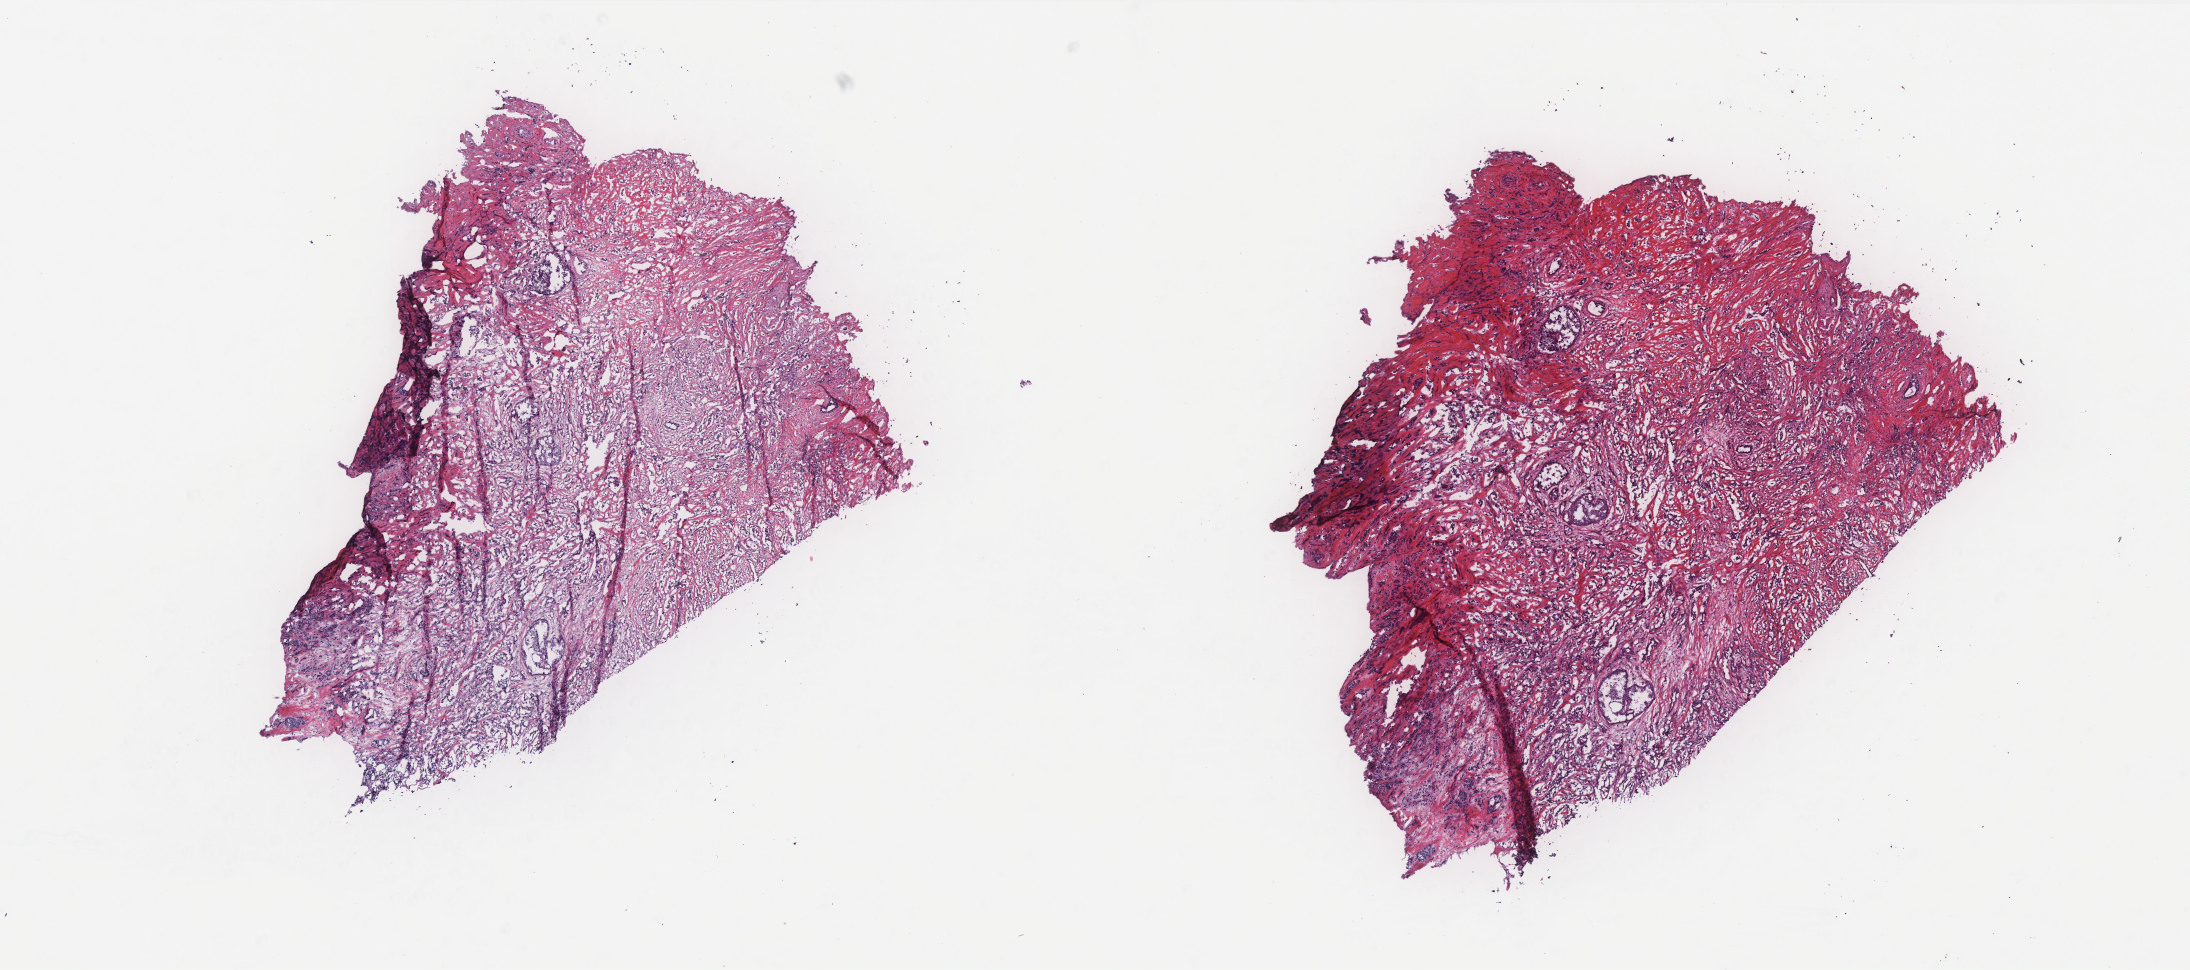
Whole-slide histology image, H&E-stained, low-resolution overview of the scanned area, about 17.6 x 7.8 mm (slide scanned at 40x). Frozen section. Primary tumour sample from the breast. Female patient; age at initial diagnosis 42 years. Slide review estimates, as recorded: tumour cells 60%, tumour nuclei 80%, normal cells 2%, stromal cells 38%, necrosis 0%. Inflammatory infiltration, as recorded: lymphocyte infiltration 3%, monocyte infiltration 0%, neutrophil infiltration 0%.
Lymph nodes positive (case pathology): 2 of 31 examined. Pathologic diagnosis: Infiltrating duct carcinoma, NOS. AJCC pathologic stage: IIB (6th edition). TNM: T2 N1a M0.